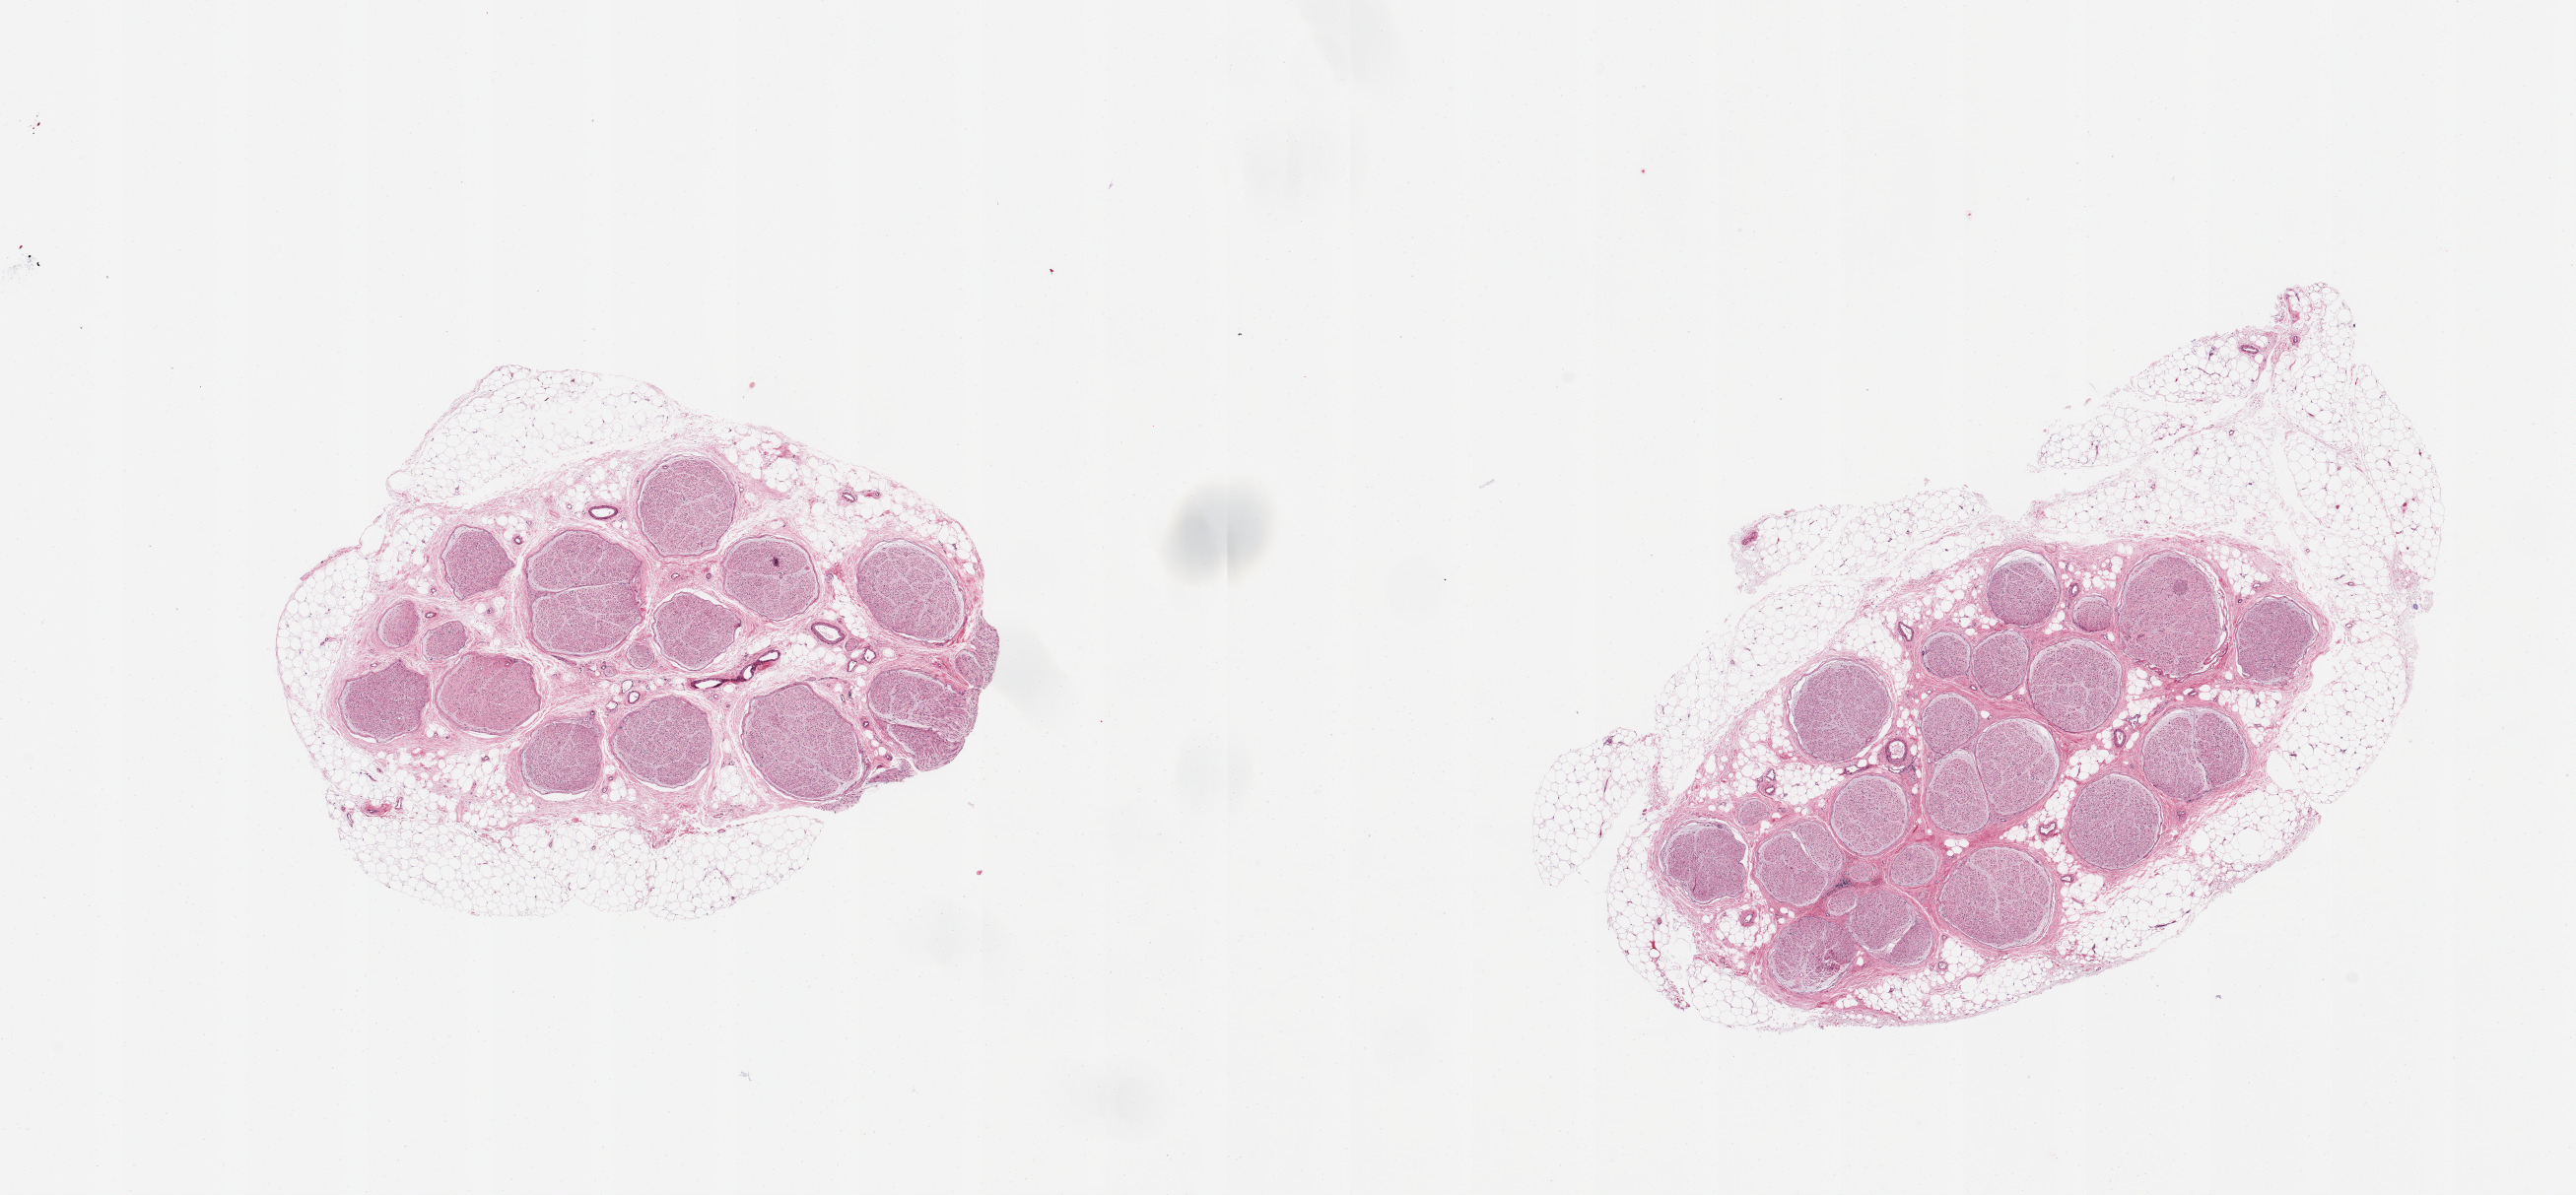
Digitized H&E-stained section, brightfield — whole scanned area (about 20.7 x 9.6 mm, acquisition: 20x scan) shown as a low-resolution overview. PAXgene-fixed paraffin-embedded (PFPE) section. Sampled site (target tissue): tibial nerve. Tissue donor sample. Female donor.
- review note (as recorded): 2 pieces, rim of adherent fat up to ~2mm